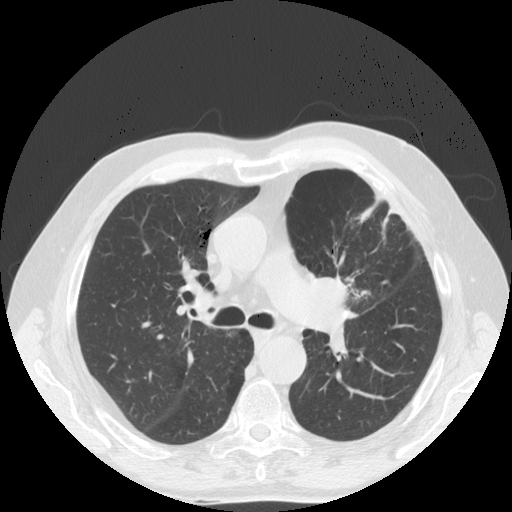
Low-dose screening chest CT, one axial slice. Position 112 of 170 along the scan axis. 140 kVp. Lung window (W 1500 / L -600 HU). 2.5 mm slice thickness. 512 × 512 image matrix, field of view 380 × 380 mm.
Outlined on this slice (manually delineated by an expert):
- lesion 1 (tumor, upper lobe of left lung): bounding box (x1, y1, x2, y2) in pixels: (309, 275, 349, 310)